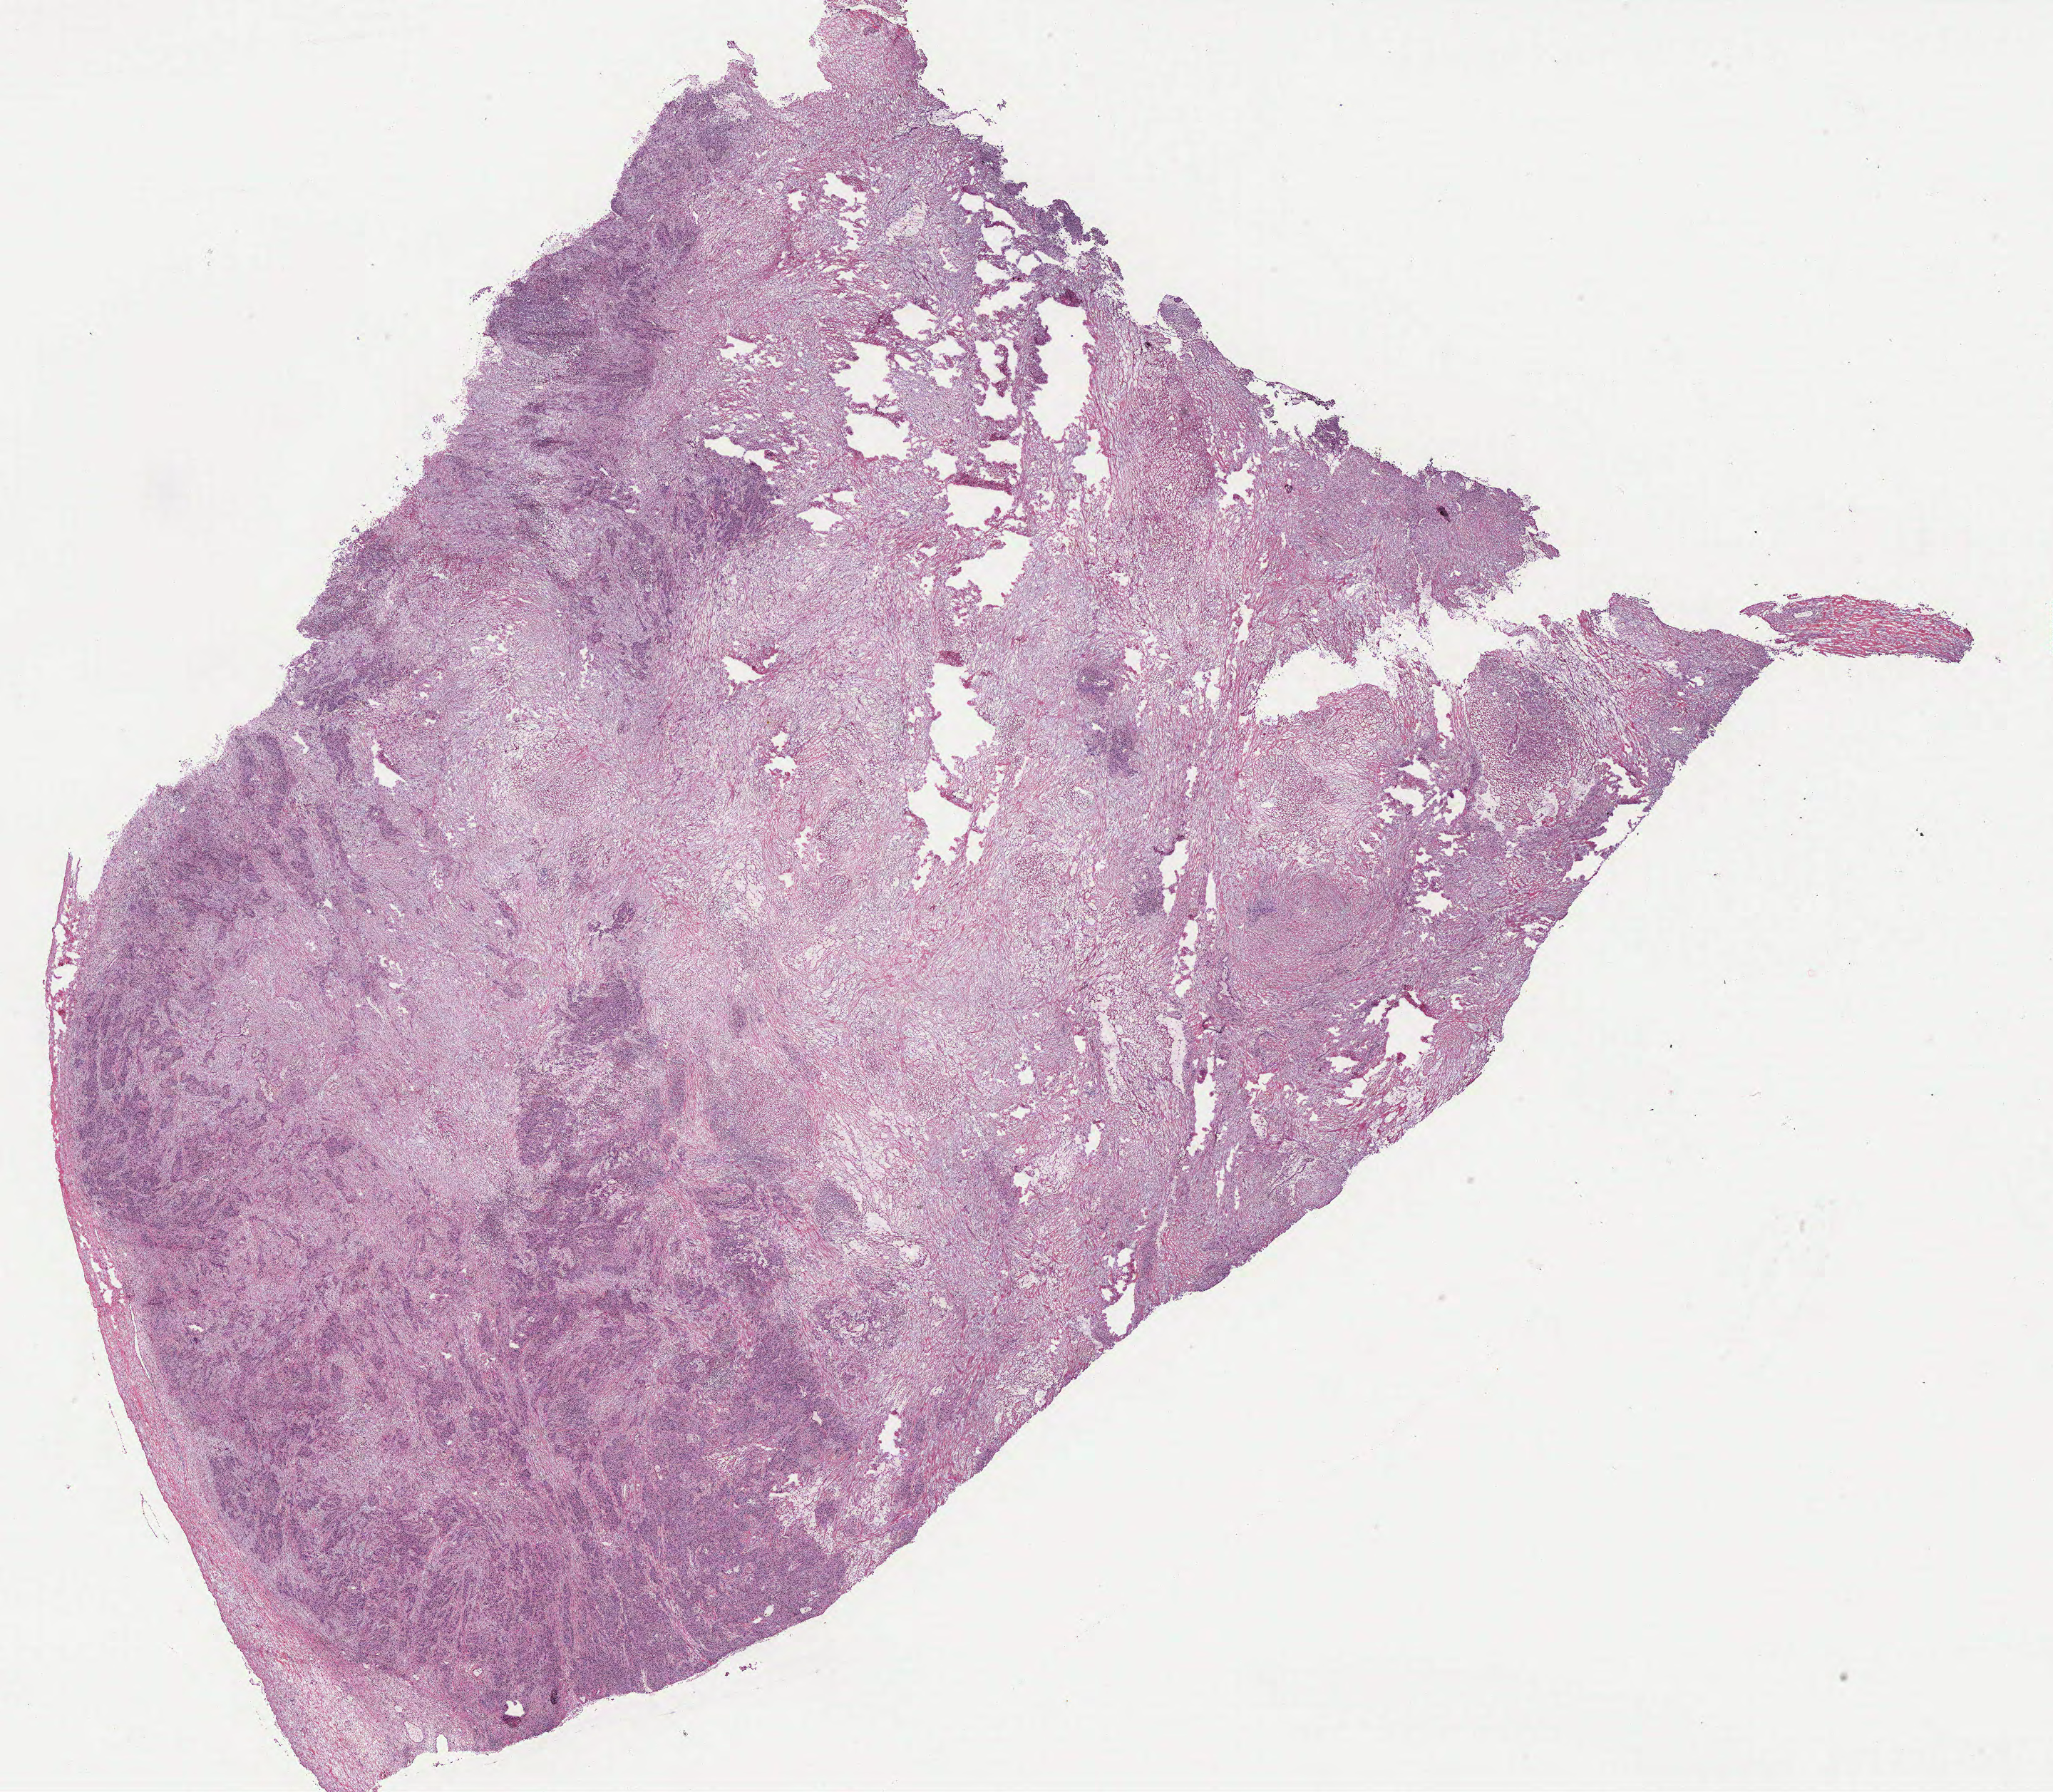
Whole-slide histology image, H&E — whole scanned area (about 23.0 x 20.1 mm, slide scanned at 40x) shown as a low-resolution overview; ovary, normal (non-tumour) tissue. 44-year-old female patient.
* this section: normal (non-tumour) tissue from the same patient
* patient diagnosis: Serous adenocarcinoma, NOS